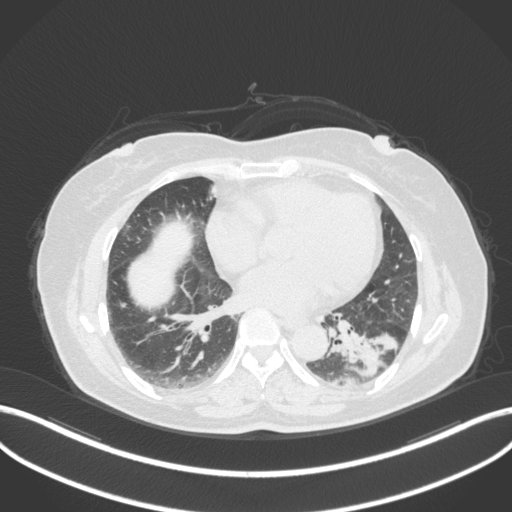
Chest CT, one axial slice; position 154 of 307 along the scan axis; 120 kVp; lung window (W 1500 / L -600 HU); 1 mm slice thickness; 512 × 512 image matrix. Patient: female, 59 years. From the clinical record (not read from this slice): clinical TNM (as recorded): T2a N0 M0; histopathological grade: G2-3.
Structures marked on this image (rectangle marked by the reading radiologist):
- lung tumour (recorded histology: adenocarcinoma): box from (x=336, y=317) to (x=401, y=394) px